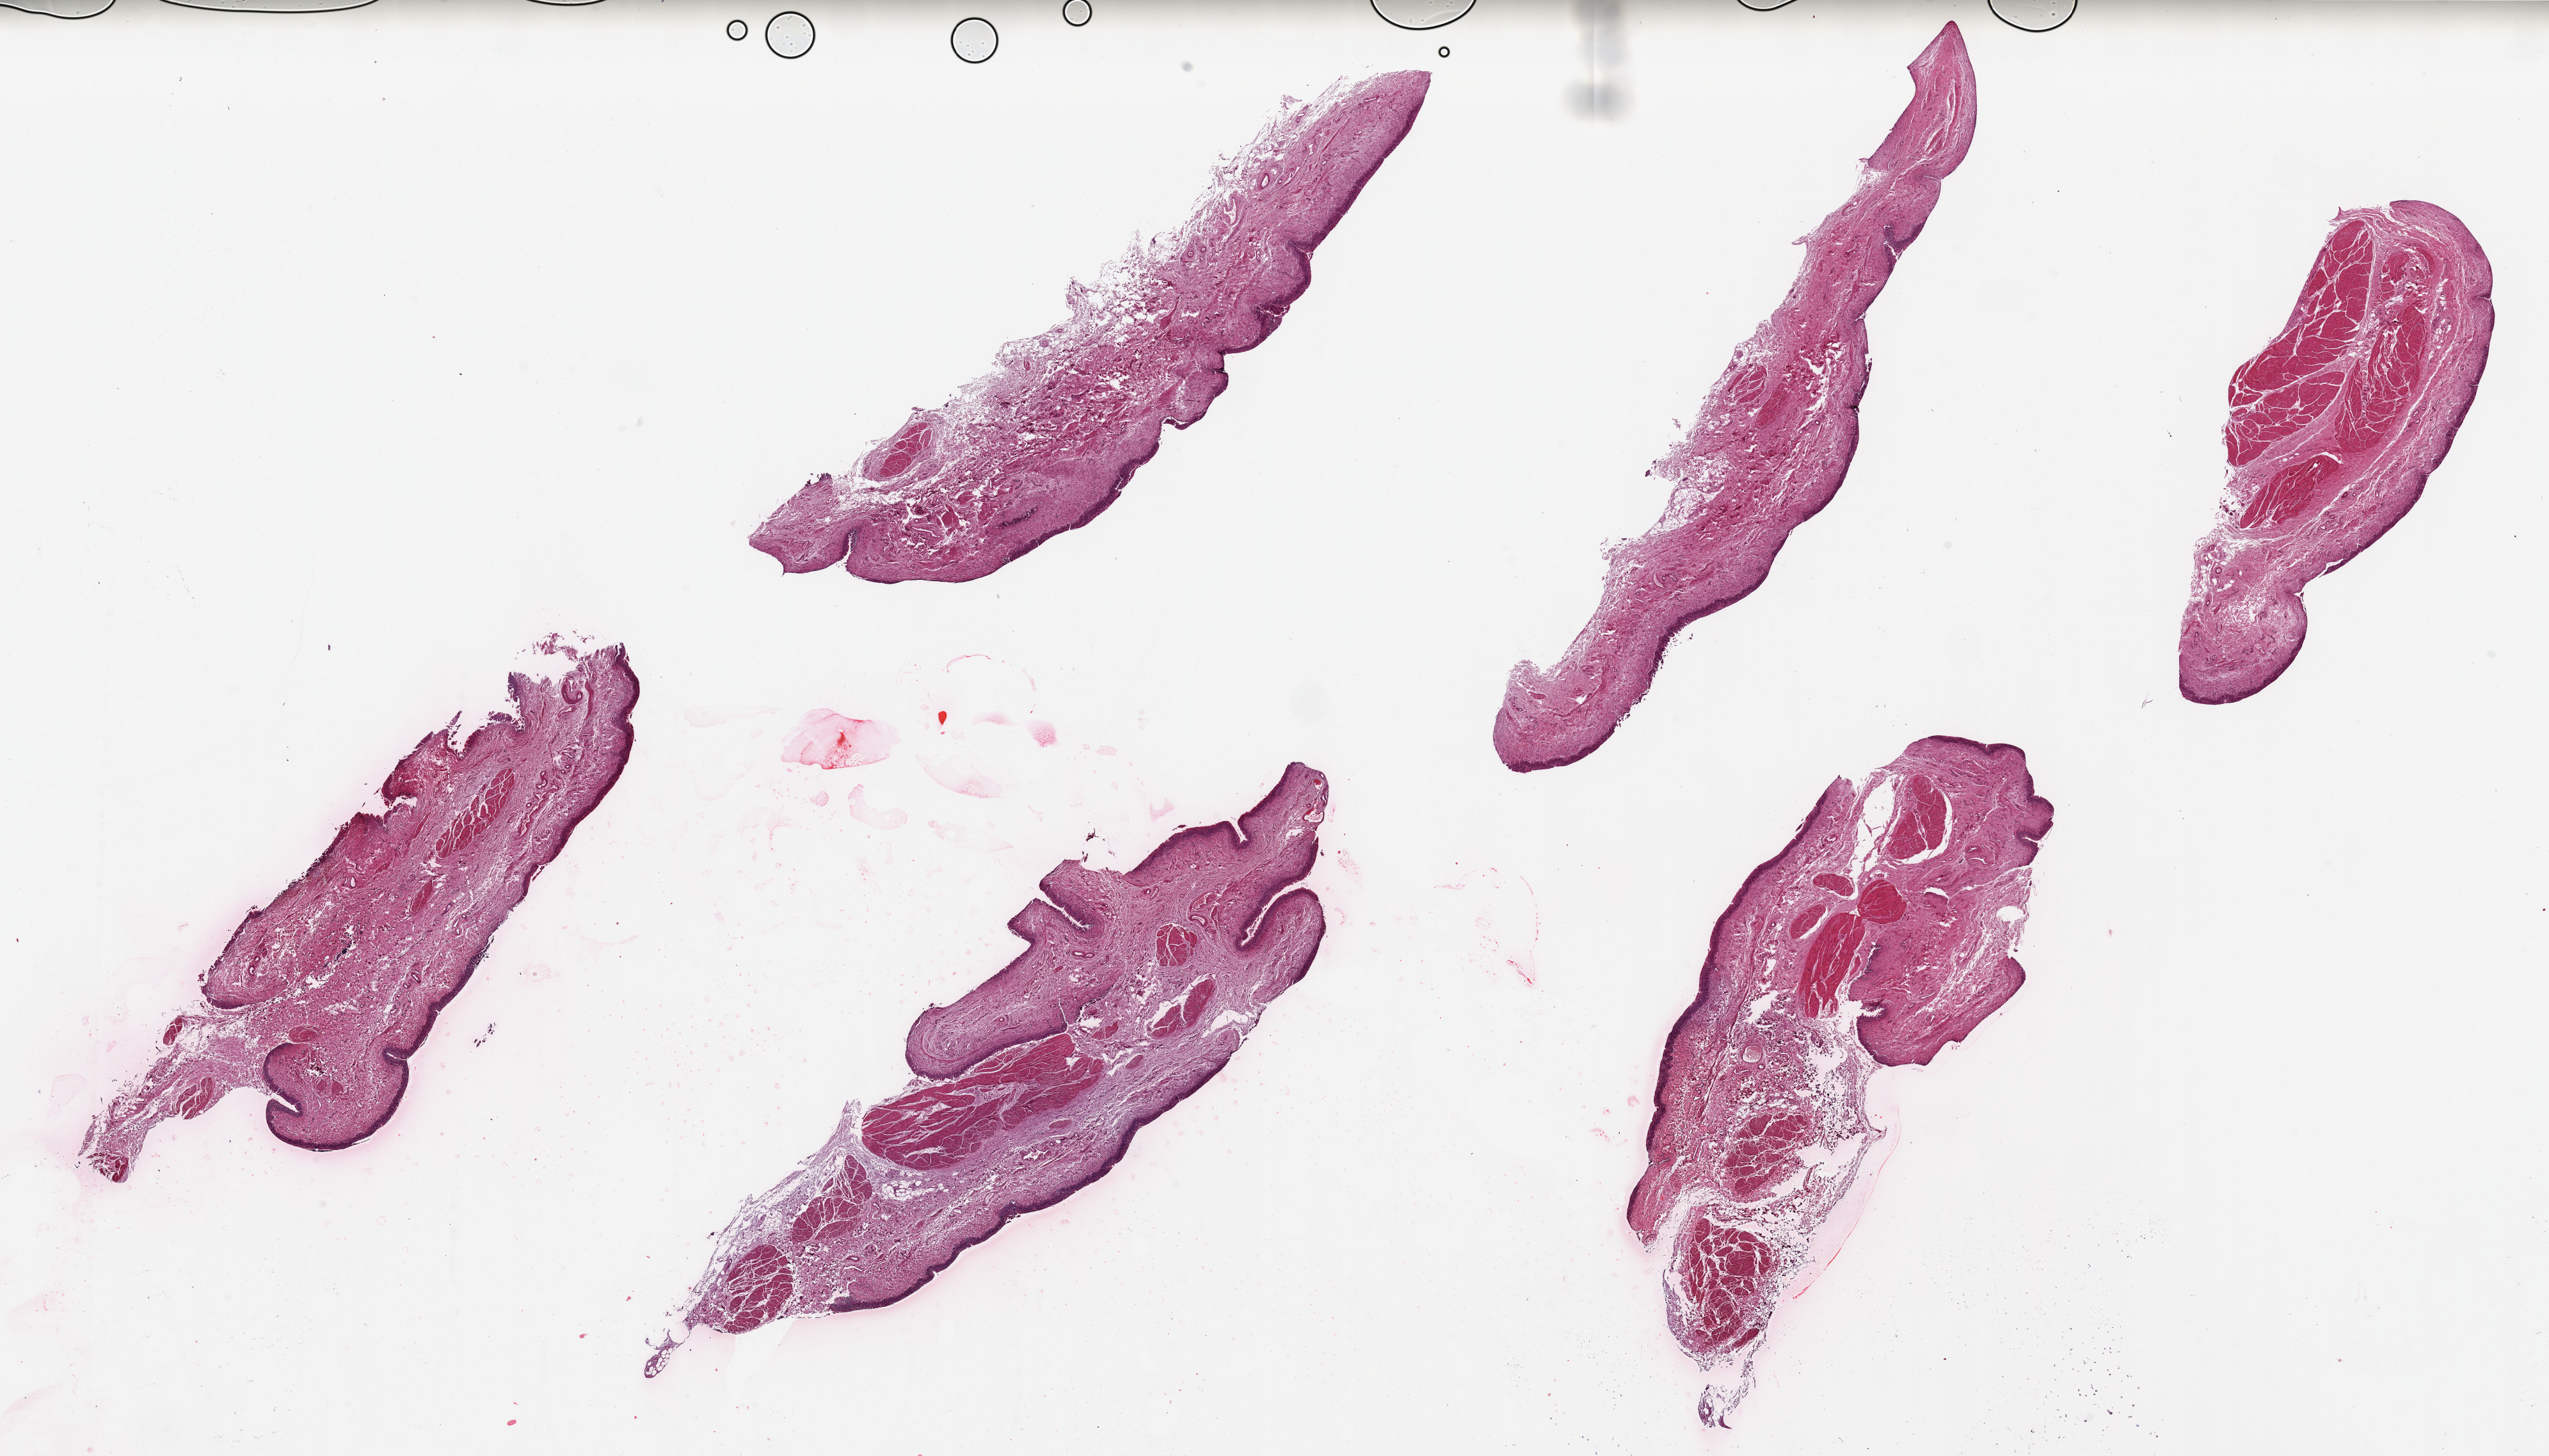
Digitized H&E-stained section — whole scanned area (about 31.5 x 18.0 mm, acquisition: 20x scan) shown as a low-resolution overview. PAXgene-fixed paraffin-embedded (PFPE) section. Section of urinary bladder (target tissue). Tissue donor sample. Donor: male.
Reviewer comment on this tissue sample: 6 pieces up to 10x3.5 mm; focally sloughed epithelium.